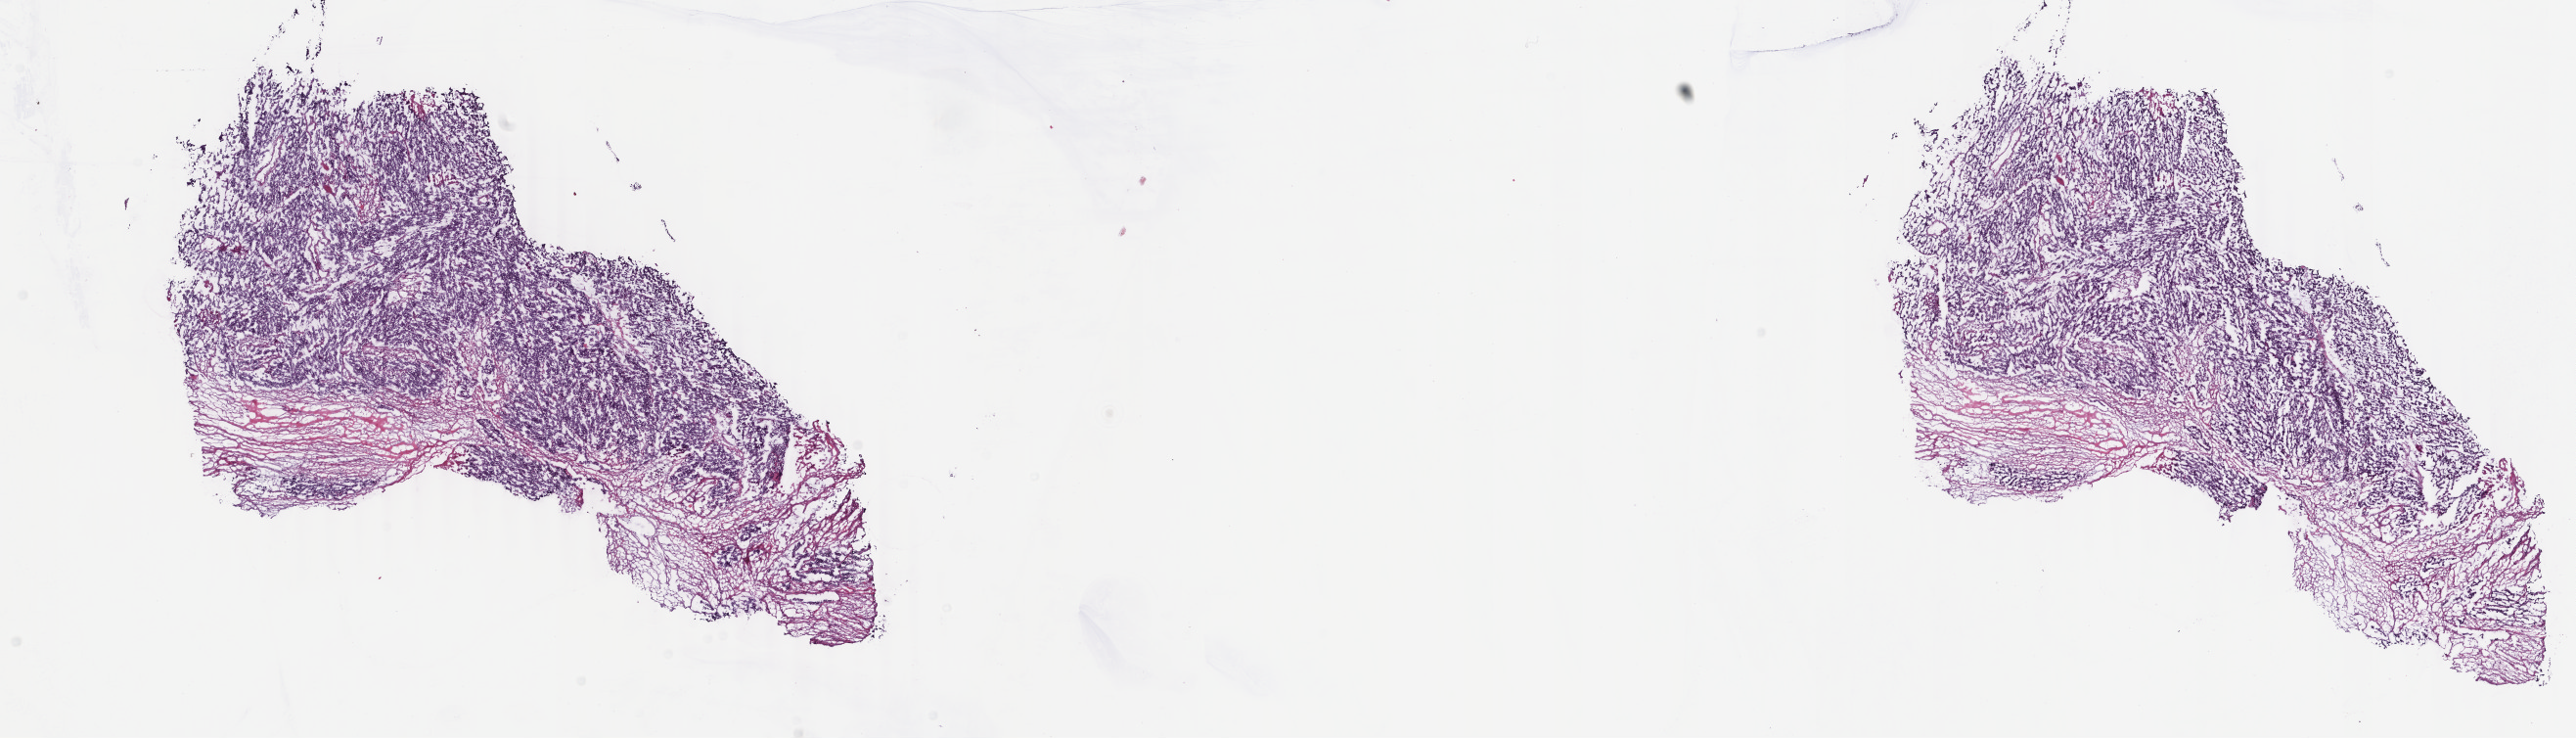
Whole-slide histology image, Hematoxylin and eosin (H&E) stained — a low-resolution overview of the entire scanned area, about 20.9 x 6.0 mm (from a 40x scan); frozen section; uterus, primary tumour sample. Female patient; age at initial diagnosis 64 years. Histologic grade: G3 (poorly differentiated). Composition of this section per pathologist review: tumour cells 67%, tumour nuclei 88%, normal cells 23%, stromal cells 2%, necrosis 8%. Inflammatory infiltration, as recorded: lymphocyte infiltration 0%, monocyte infiltration 0%, neutrophil infiltration 0%.
- FIGO stage: IIIC1
- histologic diagnosis: Endometrioid adenocarcinoma, NOS (endometrium)
- lymph nodes positive (case pathology): 1 of 22 examined